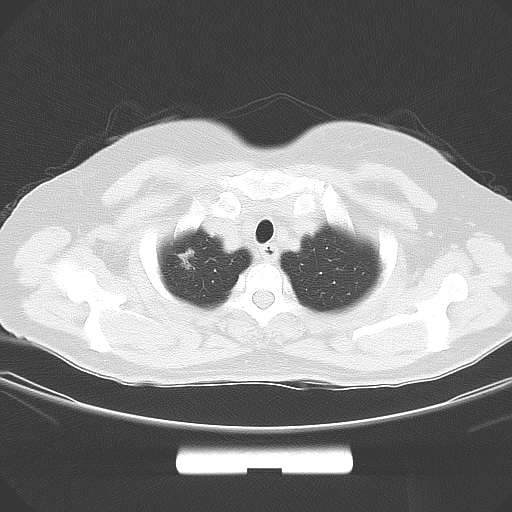
Chest CT, one axial slice. Slice 53 of 59 in the series (ordered by position). Lung window (W 1500 / L -600 HU). 5 mm slice thickness. 512 × 512 image matrix, field of view 369 × 369 mm. Patient: female, 58 years. Case-level facts recorded for this patient, not image findings: clinical TNM (as recorded): T1b N0 M0.
Outlined on this slice (rectangle marked by the reading radiologist):
- lung tumour (recorded histology: adenocarcinoma): bounding box (x1, y1, x2, y2) in pixels: (168, 241, 199, 280)